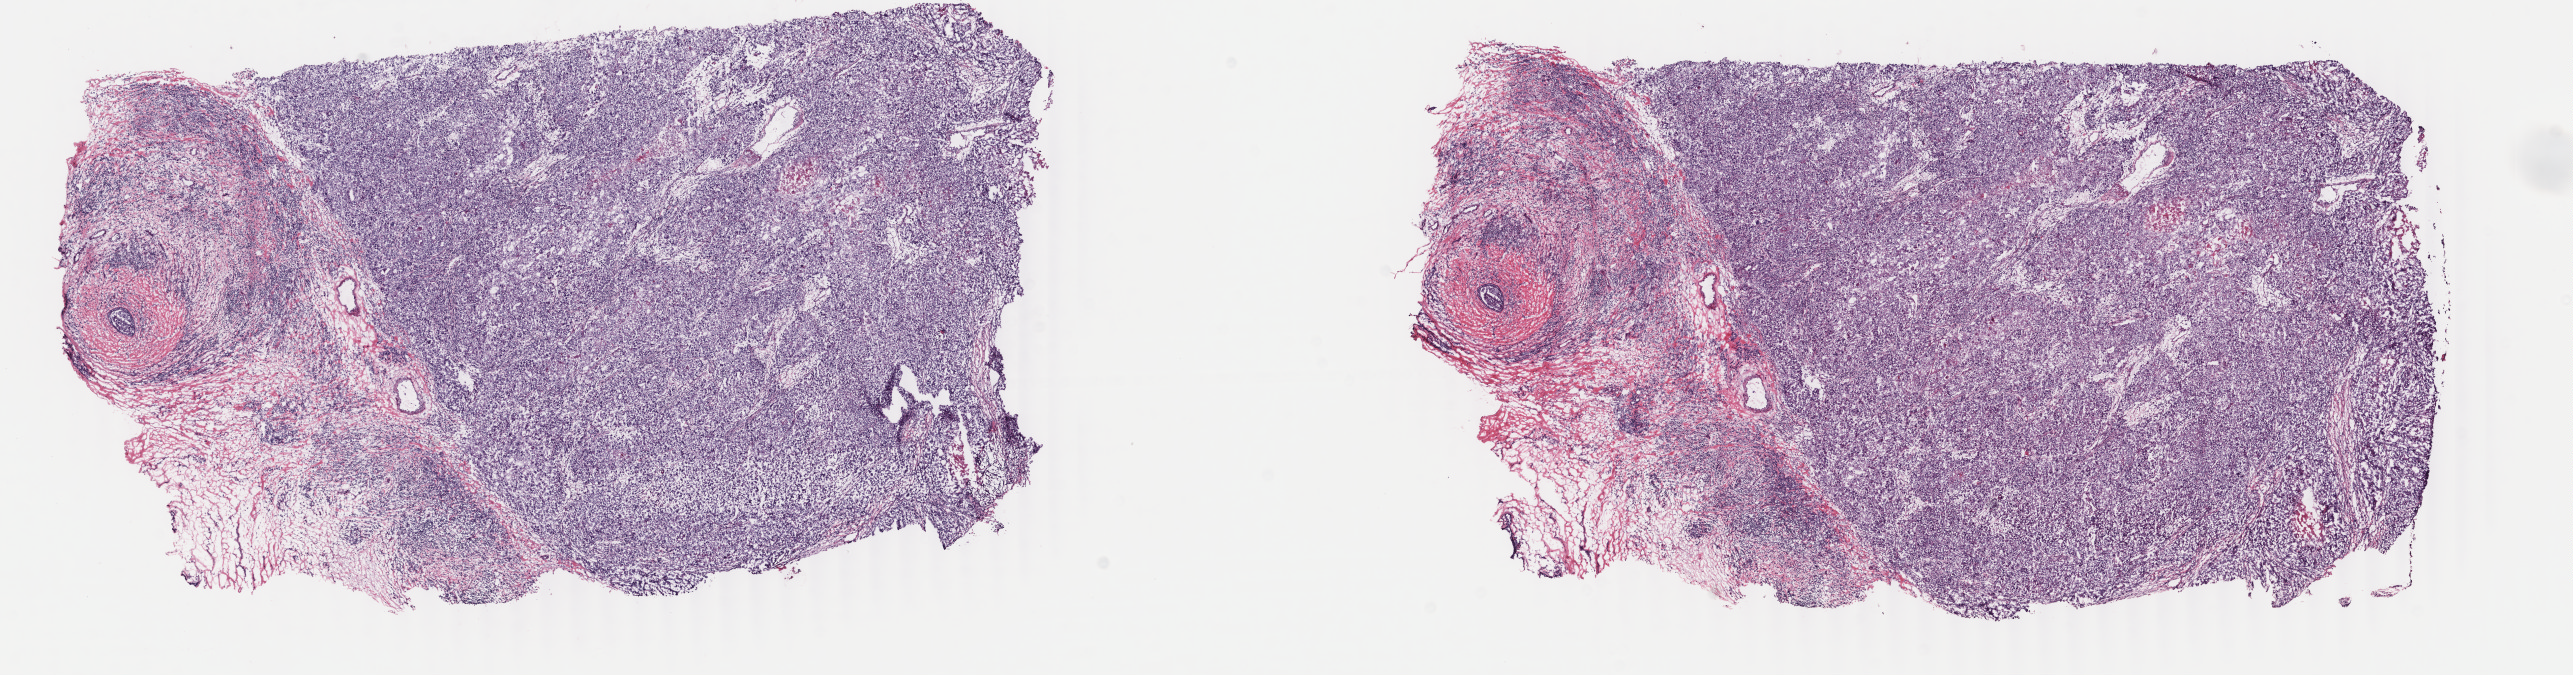
Whole-slide histology image, Hematoxylin and eosin (H&E) stained, low-resolution overview of the scanned area, about 20.5 x 5.4 mm (acquisition: 40x scan), frozen section, sample: primary tumour, breast. Female, age 73 years at initial diagnosis. Slide review estimates, as recorded: tumour cells 85%, tumour nuclei 85%, normal cells 2%, stromal cells 11%, necrosis 2%. Infiltration values recorded for this section: lymphocyte infiltration 2%, monocyte infiltration 1%, neutrophil infiltration 1%.
AJCC pathologic stage: IIB. Lymph nodes positive (case pathology): 0 of 4 examined. Laterality: left. Histologic diagnosis: Infiltrating duct carcinoma, NOS.